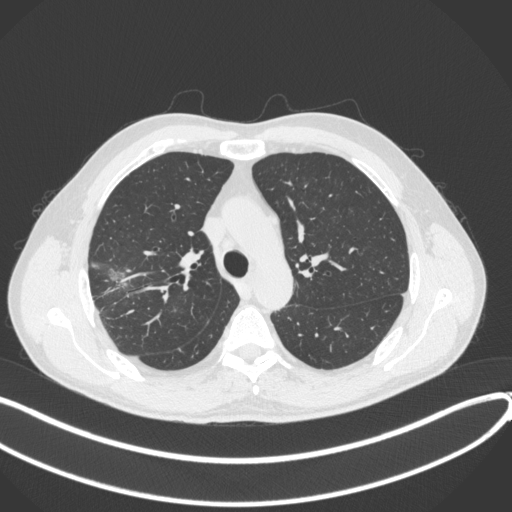
Chest CT, one axial slice. Position 296 of 381 along the scan axis. 120 kVp. Lung window (W 1500 / L -600 HU). 512 × 512 image matrix, field of view 400 × 400 mm. Patient: male, 62 years. From the clinical record (not read from this slice): clinical TNM (as recorded): T1c N0 M0; histopathological grade: G2-3.
Outlined on this slice (bounding box drawn by a radiologist):
- lung tumour (recorded histology: adenocarcinoma): box from (x=104, y=266) to (x=129, y=292) px